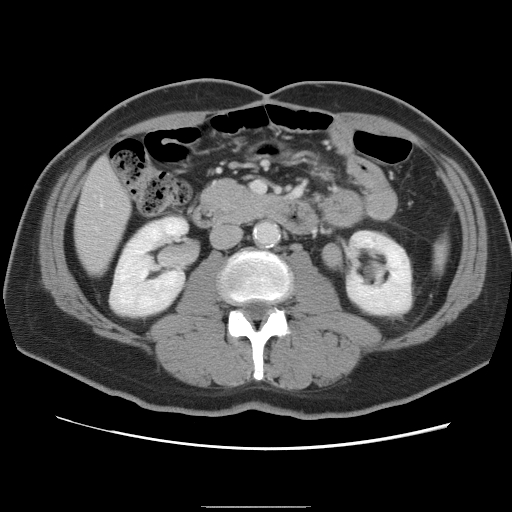
Contrast-enhanced abdominal CT, one axial slice. Slice 24 of 87 in the series (ordered by position). 120 kVp. Intravenous contrast given. Soft-tissue window (W 400 / L 40 HU). 5 mm slice thickness. 512 × 512 image matrix, field of view 363 × 363 mm. Male patient, age 63 years. From the clinical record (not read from this slice): diagnosis: colorectal cancer liver metastases, imaged before liver resection; multiple liver metastases: no; largest metastasis: 9 cm.
Outlined on this slice (manually delineated by an expert):
- liver: box from (x=76, y=160) to (x=130, y=274) px
- planned liver remnant (the part of the liver to remain after resection): (x=75, y=160)–(x=130, y=274)